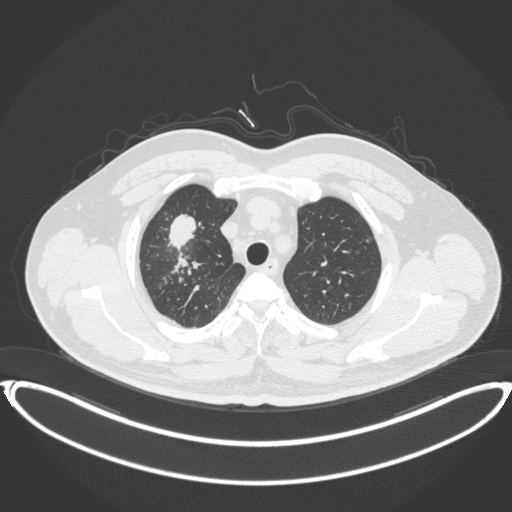
Chest CT, one axial slice; position 315 of 399 along the scan axis; 120 kVp; lung window (W 1500 / L -600 HU); 1 mm slice thickness; 512 × 512 image matrix, field of view 445 × 445 mm. Patient: male, 53 years. Case-level facts recorded for this patient, not image findings: clinical TNM (as recorded): T2a N0 M0.
Structures marked on this image (rectangle marked by the reading radiologist):
- lung tumour (recorded histology: adenocarcinoma): box from (x=164, y=210) to (x=201, y=251) px